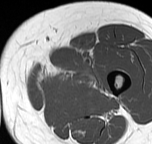
MRI of an extremity soft-tissue mass, one axial slice; MR volume resampled by the dataset authors to the PET/CT grid (not the native acquisition matrix); 3.27 mm slice thickness; 152 × 144 image matrix, field of view 148 × 141 mm. Female patient. From the clinical record (not read from this slice): histological type: pleiomorphic leiomyosarcoma; grade: intermediate; site of the primary tumour: left thigh.
Annotated regions visible in this slice (expert contour drawn on MRI and transferred to this co-registered scan by the dataset authors):
- gross tumour volume including surrounding oedema: box from (x=38, y=62) to (x=101, y=95) px